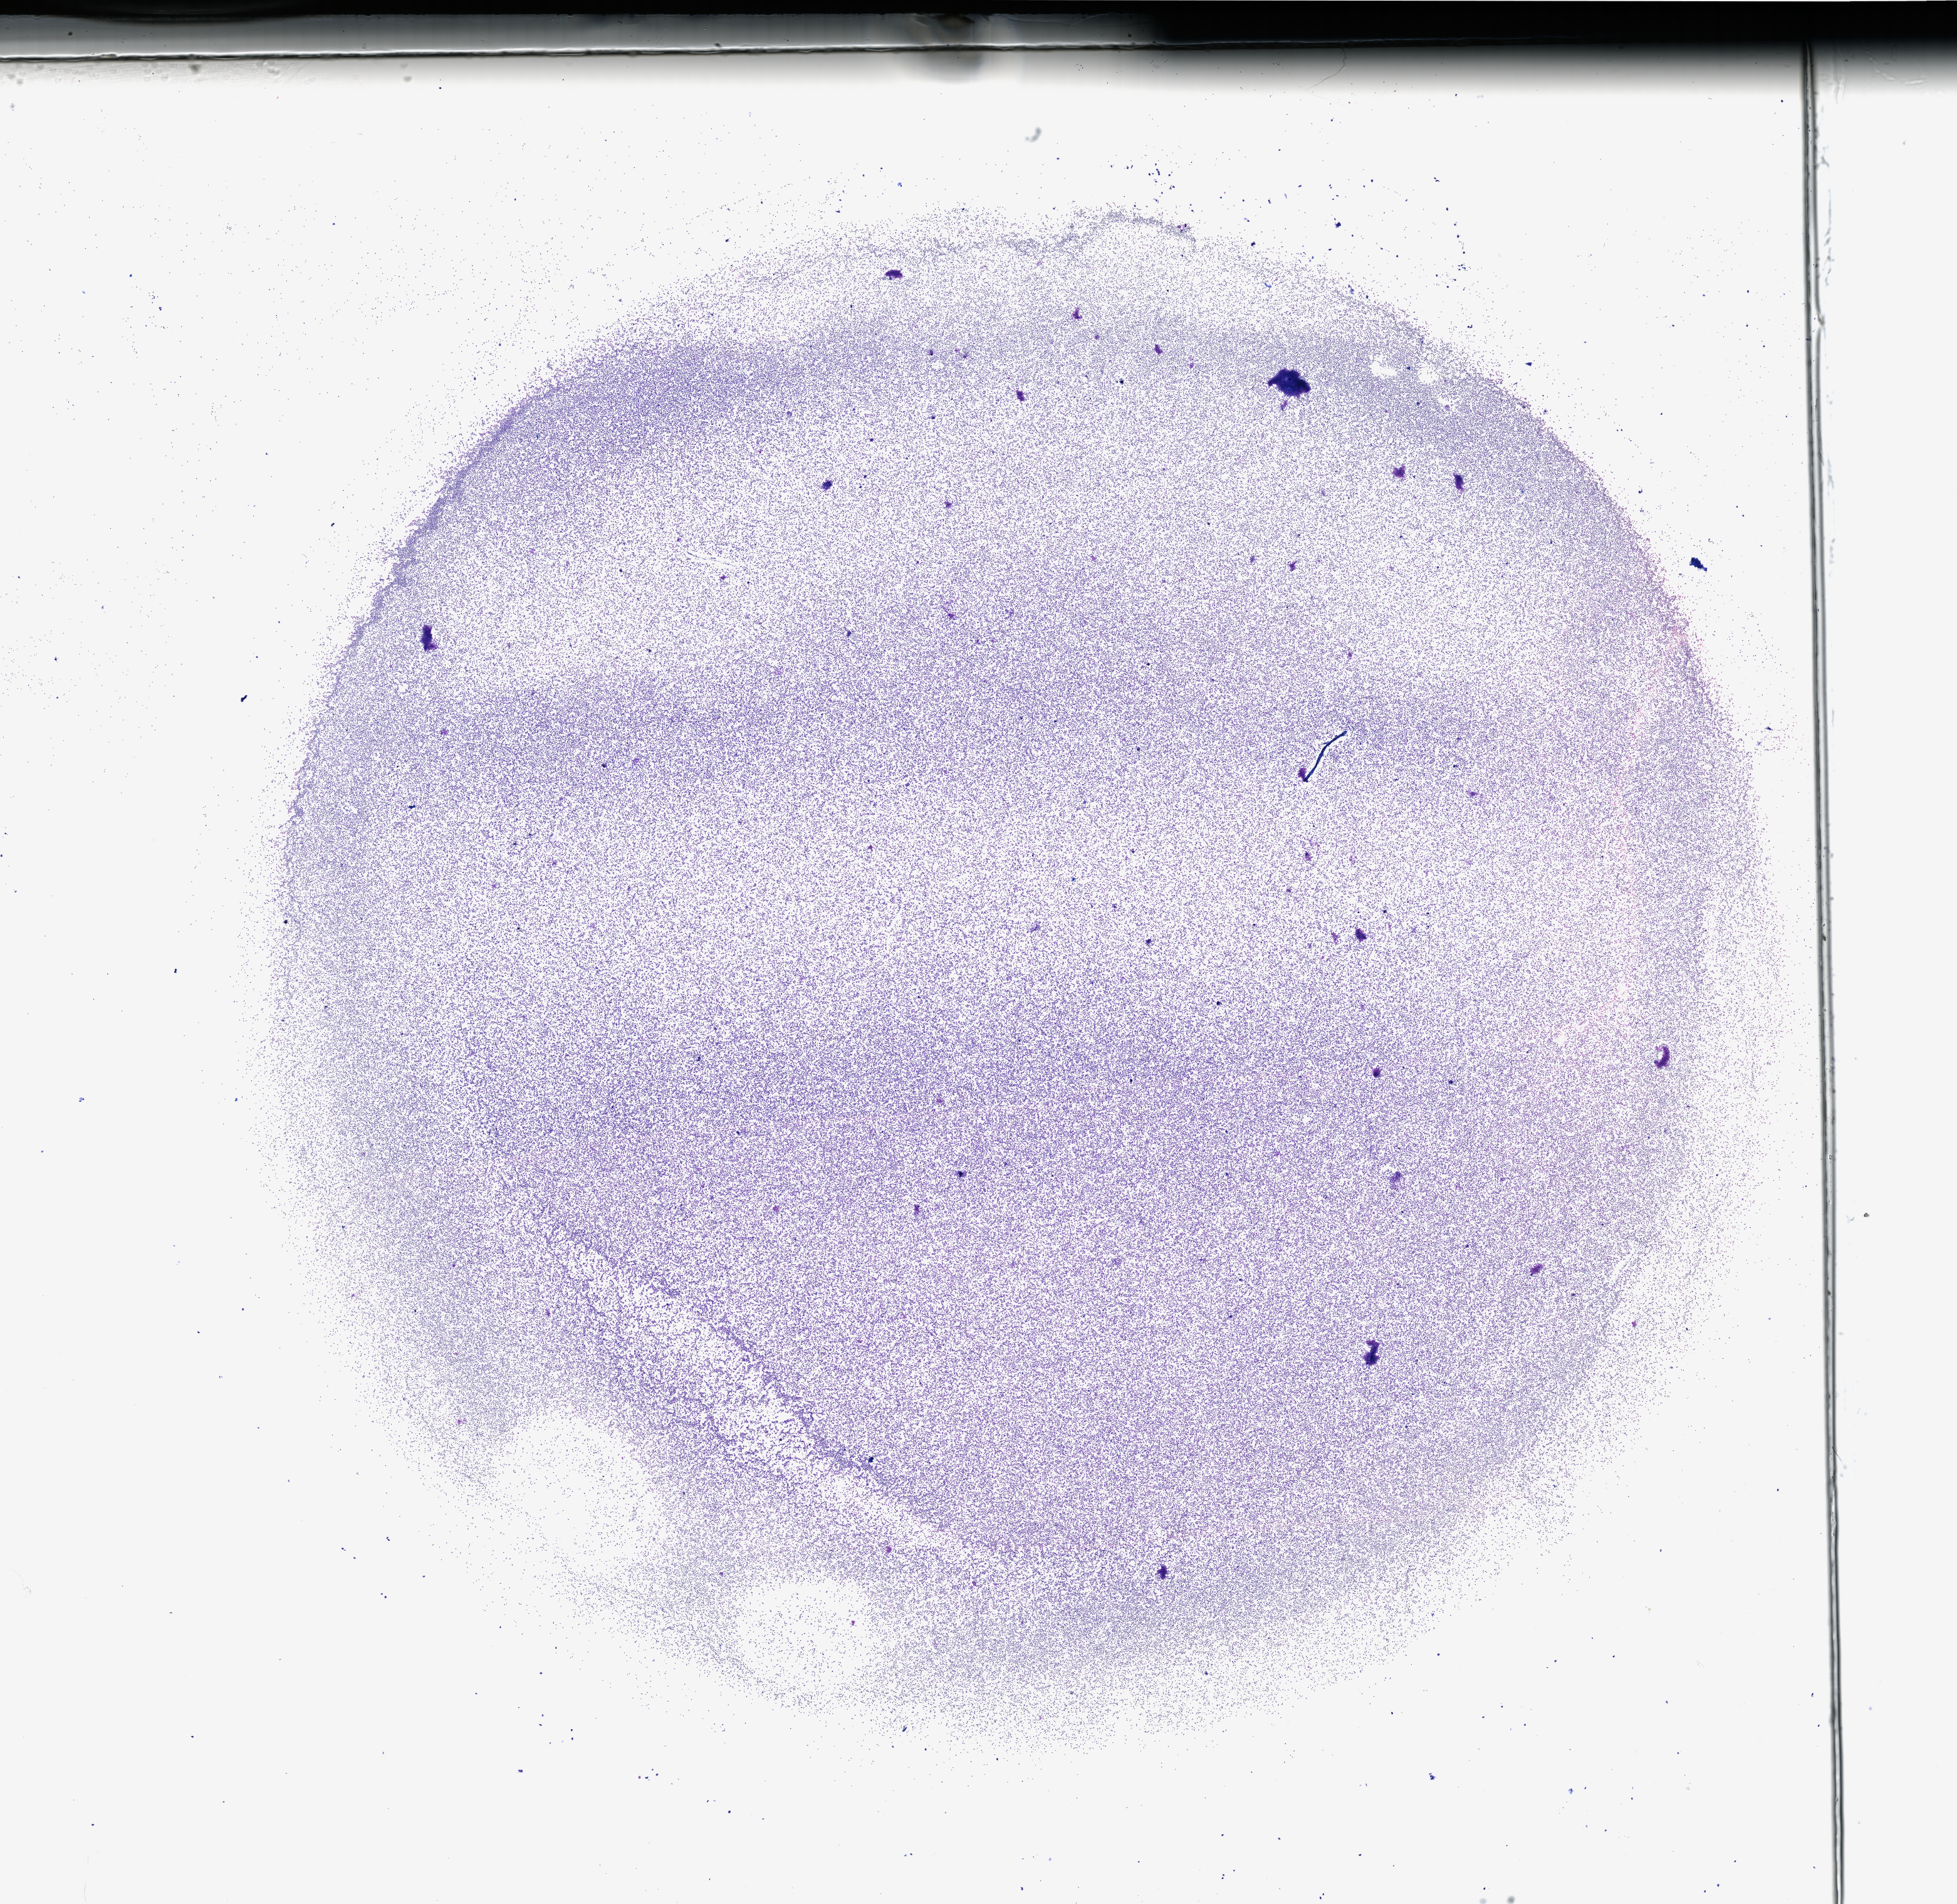
Whole-slide histology image, H&E-stained — a low-resolution overview of the entire scanned area, about 24.7 x 24.0 mm (from a 40x scan); bone marrow (leukaemic) sample. Patient: female, age 64 years. Blasts: 90%.
Diagnosis: Acute Myeloid Leukemia. WHO classification: Acute myelomonocytic leukemia. FAB classification: M4.